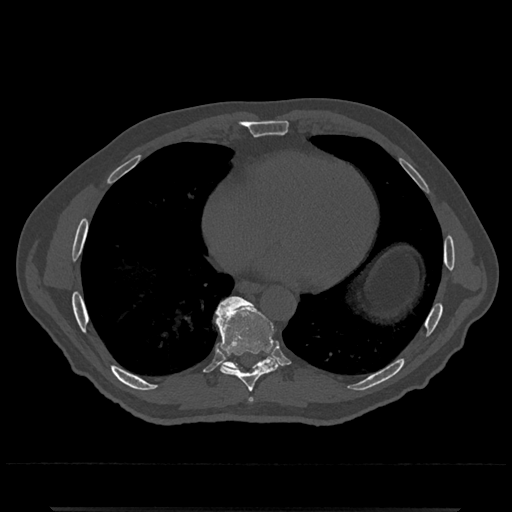
CT including the spine, one axial slice. Position 651 of 797 along the scan axis. 120 kVp. Bone window (W 1800 / L 400 HU). 0.5 mm slice thickness. 512 × 512 image matrix, field of view 393 × 393 mm. Male patient, age 67 years. From the clinical record (not read from this slice): primary cancer: prostate.
Annotated regions visible in this slice (semi-automatically segmented with operator editing):
- T7 vertebra: box from (x=250, y=398) to (x=253, y=401) px
- T8 vertebra: (x=215, y=302)–(x=280, y=392)
- T9 vertebra: (x=214, y=296)–(x=277, y=371)